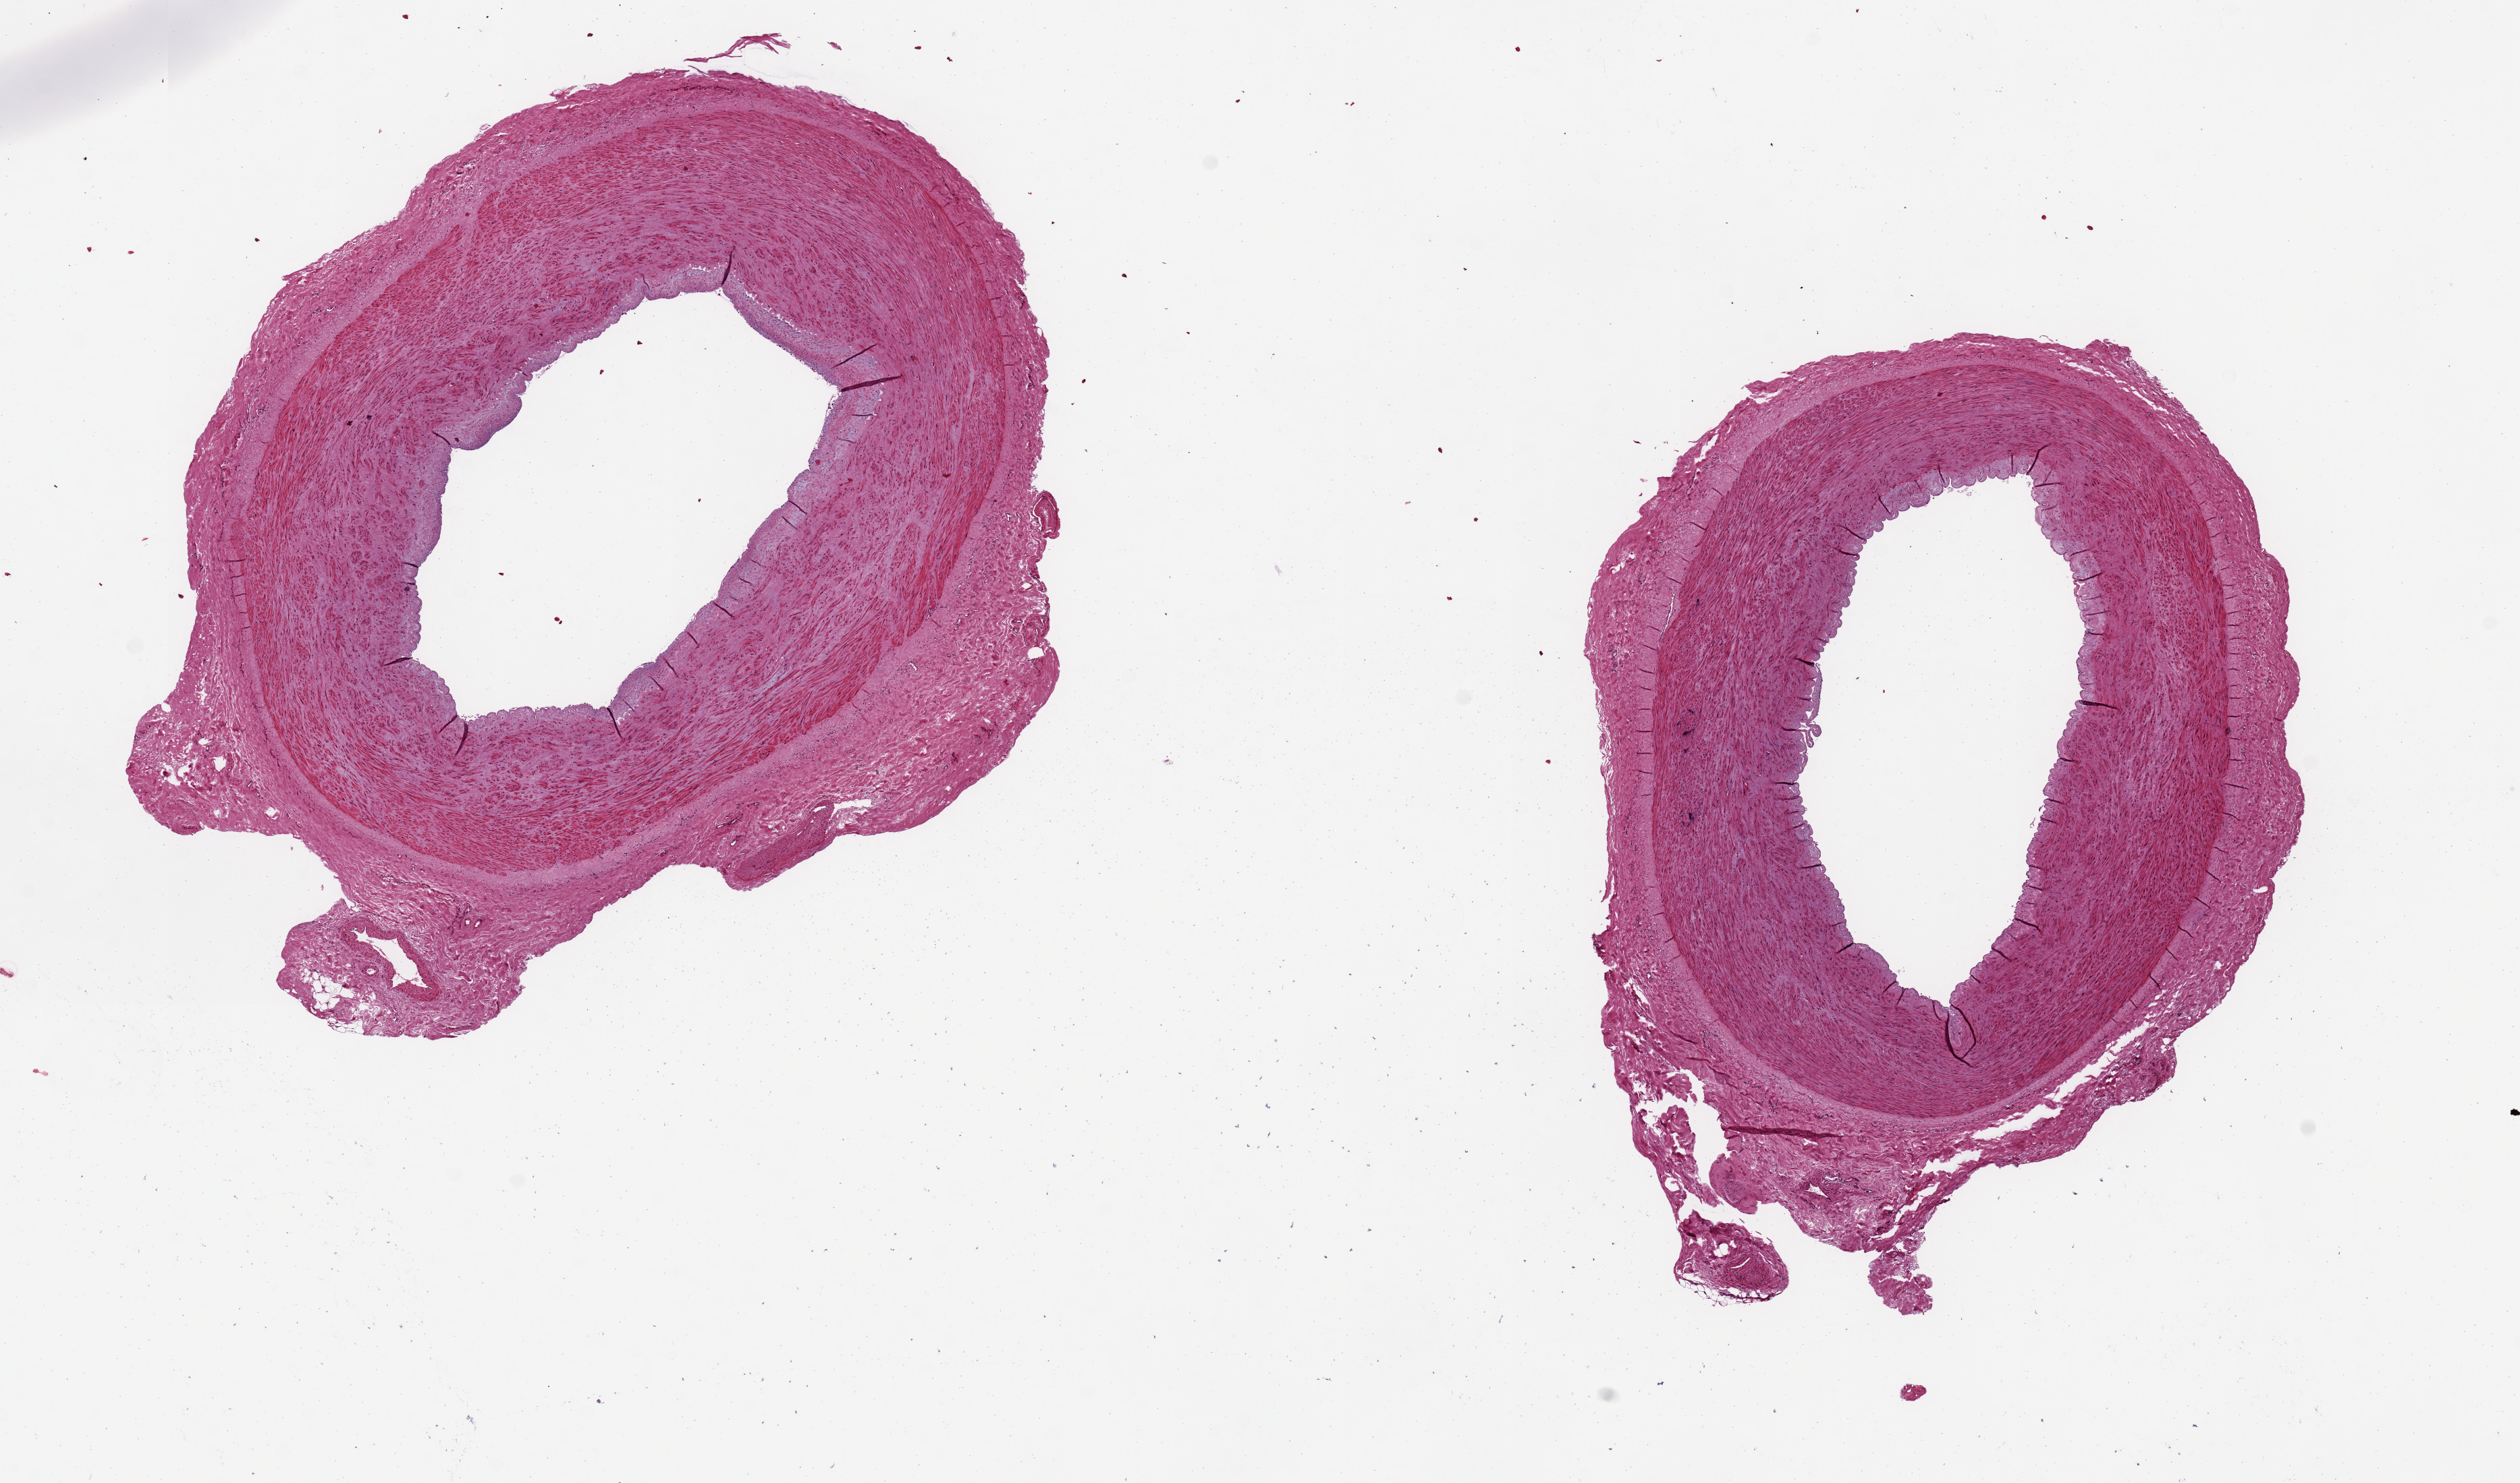
Whole-slide image, haematoxylin and eosin stain, a low-resolution overview of the entire scanned area, about 14.8 x 8.7 mm (acquisition: 20x scan). PAXgene-fixed, paraffin-embedded tissue. Target tissue: tibial artery. Tissue donor sample. Male donor.
Review note (as recorded): 2 pieces of 5mm artery; clean, no adipose; no sclerosis.